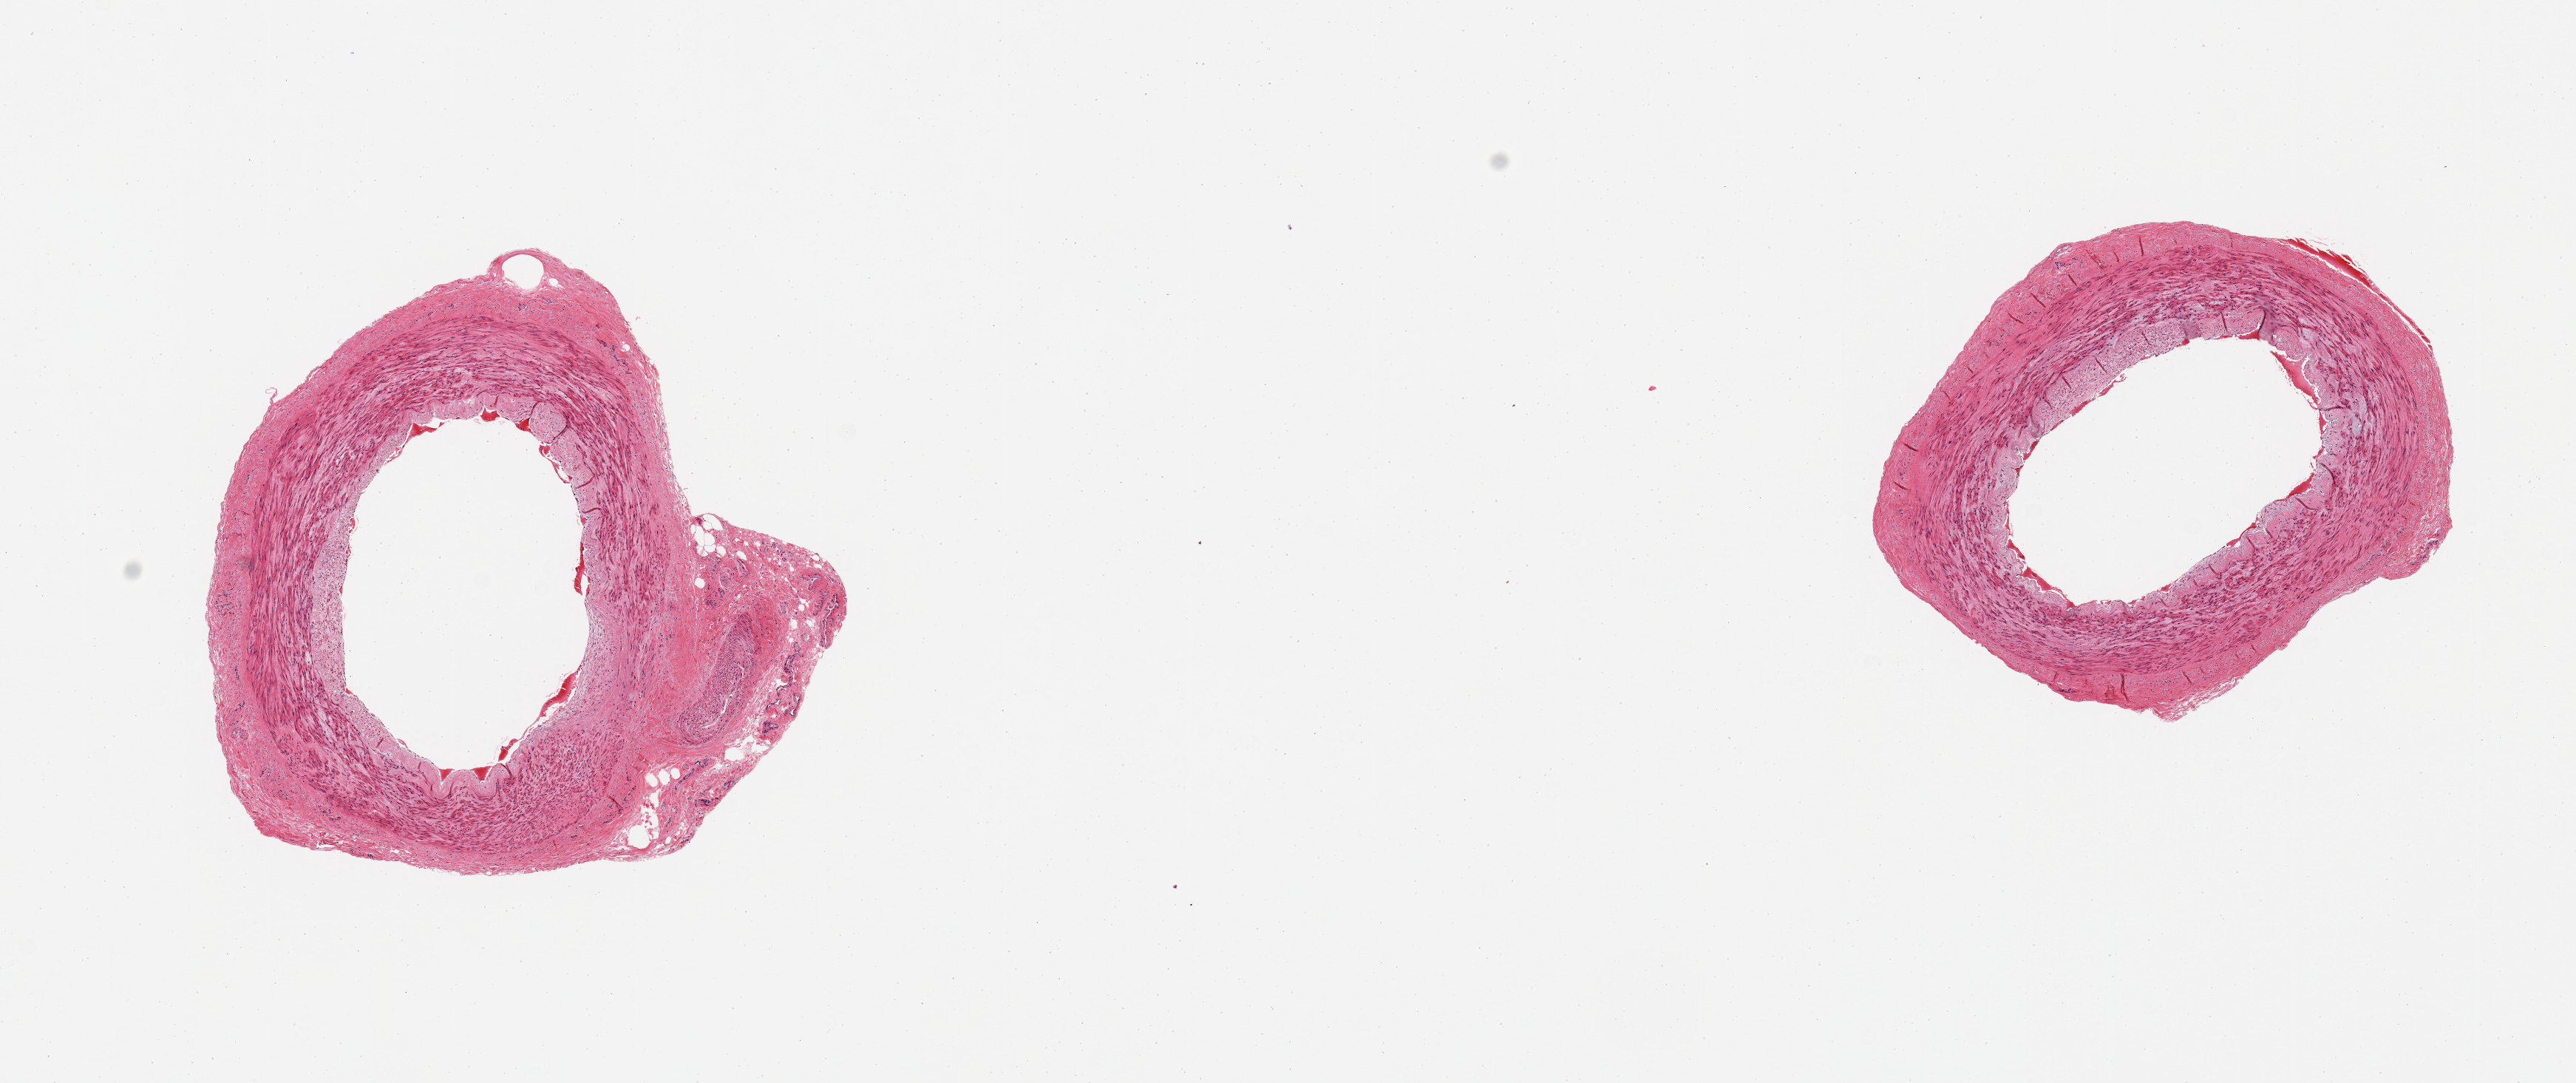
Digitized haematoxylin and eosin-stained section, brightfield — shown as a low-resolution overview of the whole scanned area (about 13.8 x 5.8 mm). PAXgene-fixed paraffin-embedded (PFPE) section. Section of tibial artery (target tissue). Tissue donor sample. Donor: male.
Pathologist's review note for this sample: 2 pieces; intimal thickening.